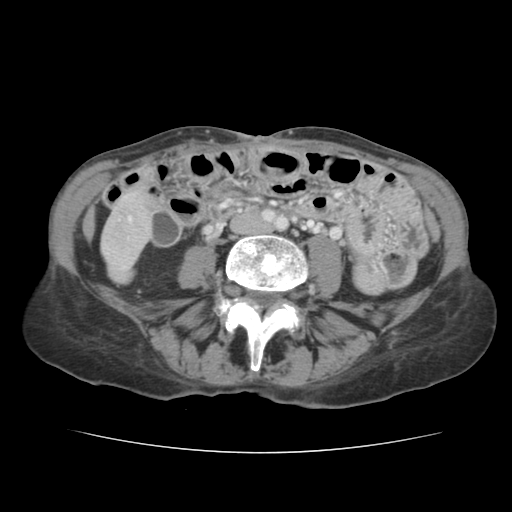
Contrast-enhanced abdominal CT, one axial slice. Position 19 of 136 along the scan axis. Soft-tissue window (W 400 / L 40 HU). 2.5 mm slice thickness. 512 × 512 image matrix, field of view 319 × 319 mm. Female patient, age 77 years. From the clinical record (not read from this slice): diagnosis: colorectal cancer liver metastases, imaged before liver resection.
Annotated regions visible in this slice (expert manual segmentation):
- liver: bounding box <103,192,149,275> (left, top, right, bottom; pixels)